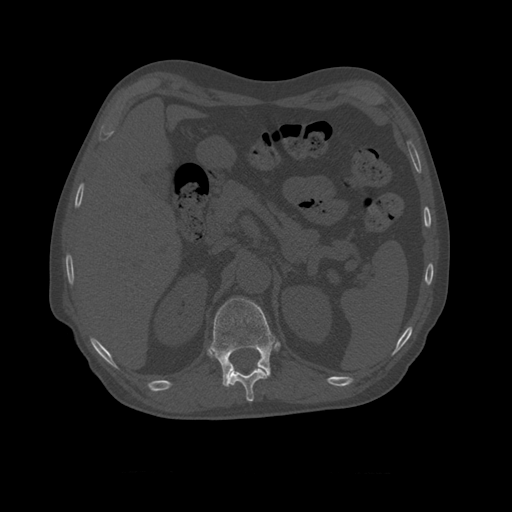
CT including the spine, one axial slice; 120 kVp; bone window (W 1800 / L 400 HU); 1.25 mm slice thickness; 512 × 512 image matrix, field of view 405 × 405 mm. Patient age 75 years. From the clinical record (not read from this slice): primary cancer: prostate.
Annotated regions visible in this slice (semi-automatic segmentation, software-assisted and operator-edited):
- T10 vertebra: box from (x=211, y=347) to (x=274, y=402) px
- T11 vertebra: (x=211, y=298)–(x=276, y=388)